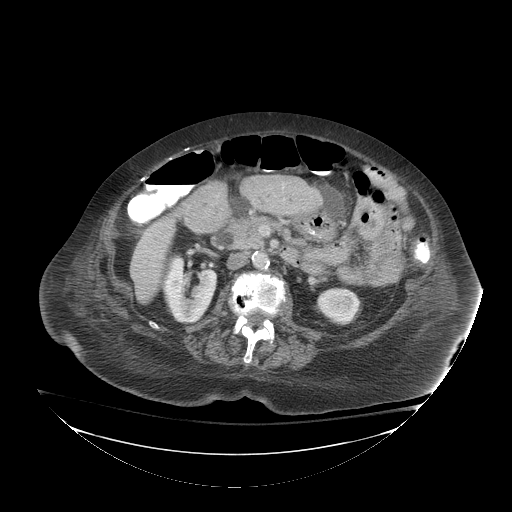
Contrast-enhanced abdominal CT (liver protocol), one axial slice; position 27 of 81 along the scan axis; reconstruction kernel STANDARD; 140 kVp; soft-tissue window (W 400 / L 40 HU); 2.5 mm slice thickness; 512 × 512 image matrix, field of view 500 × 500 mm. From the clinical record (not read from this slice): diagnosis: hepatocellular carcinoma (patient treated with transarterial chemoembolisation; whether this scan precedes or follows treatment is not stated here); TNM stage (as recorded): Stage-I; Child-Pugh class: B.
Annotated regions visible in this slice (semi-automatically segmented with operator editing):
- liver parenchyma outside the tumour (the mass and vessels are separate outlines, so this box may not span the whole liver): bounding box (x1, y1, x2, y2) in pixels: (130, 216, 174, 300)